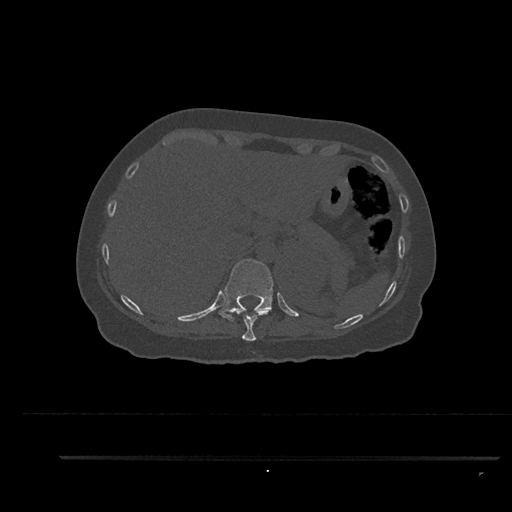
CT including the spine, one axial slice; slice 334 of 797 in the series (ordered by position); reconstruction kernel Br40s/3; 120 kVp; bone window (W 1800 / L 400 HU); 0.5 mm slice thickness; 512 × 512 image matrix, field of view 408 × 408 mm. Female patient, age 44 years. Case-level facts recorded for this patient, not image findings: primary cancer: renal; vertebrae with lytic lesions (as recorded): L1.
Structures marked on this image (semi-automatically segmented with operator editing):
- T10 vertebra: bounding box (x1, y1, x2, y2) in pixels: (232, 308, 261, 341)
- T11 vertebra: (219, 259, 274, 322)